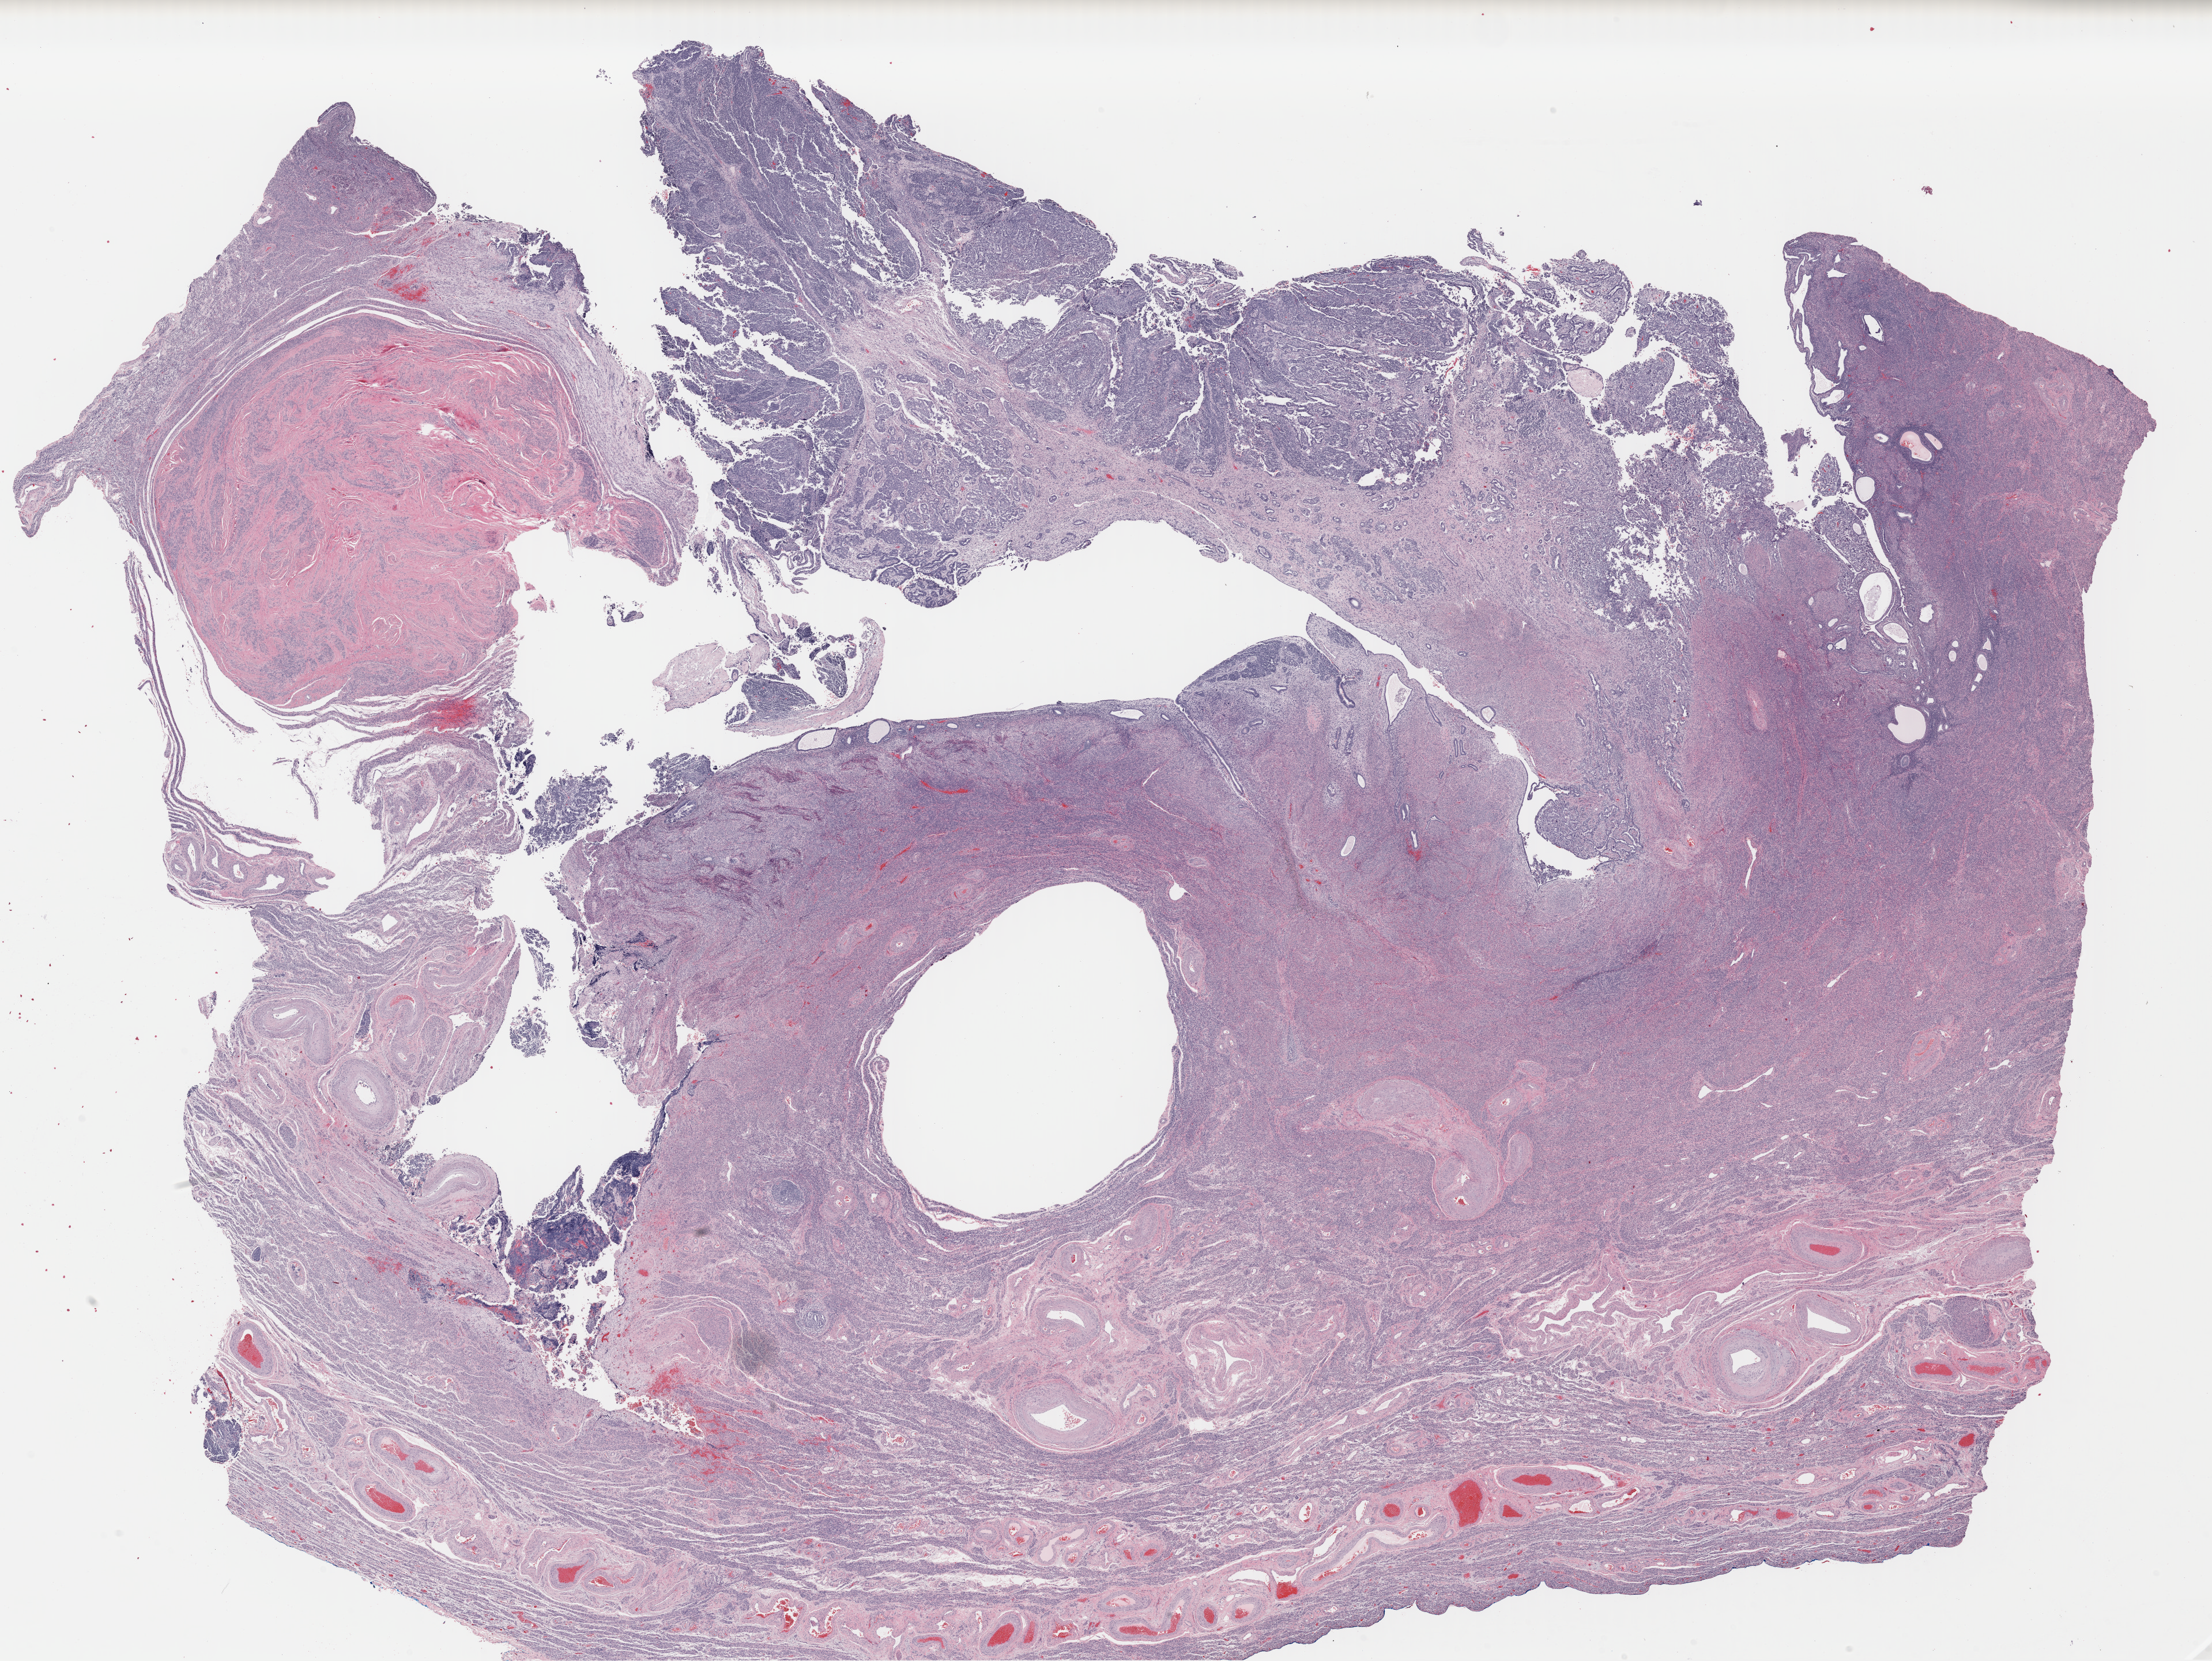
Whole-slide histology image, H&E, whole scanned area (about 30.2 x 22.6 mm) shown as a low-resolution overview; formalin-fixed paraffin-embedded (FFPE) diagnostic section; sample: primary tumour, uterus. Female, age 65 years at initial diagnosis.
• FIGO stage: IB
• pathologic diagnosis: Mullerian mixed tumor (endometrium)